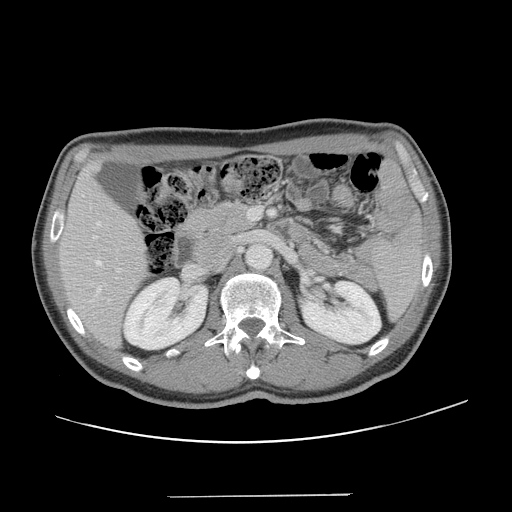
Contrast-enhanced abdominal CT, one axial slice. Slice 68 of 131 in the series (ordered by position). 120 kVp. Soft-tissue window (W 400 / L 40 HU). 2.5 mm slice thickness. 512 × 512 image matrix, field of view 403 × 403 mm. Male patient, age 60 years. From the clinical record (not read from this slice): diagnosis: colorectal cancer liver metastases, imaged before liver resection; multiple liver metastases: no; largest metastasis: 2.5 cm; chemotherapy before resection: no.
Outlined on this slice (expert manual segmentation):
- hepatic veins: bounding box (x1, y1, x2, y2) in pixels: (96, 222, 101, 292)
- liver: (60, 166, 149, 347)
- planned liver remnant (the part of the liver to remain after resection): (60, 166, 148, 347)